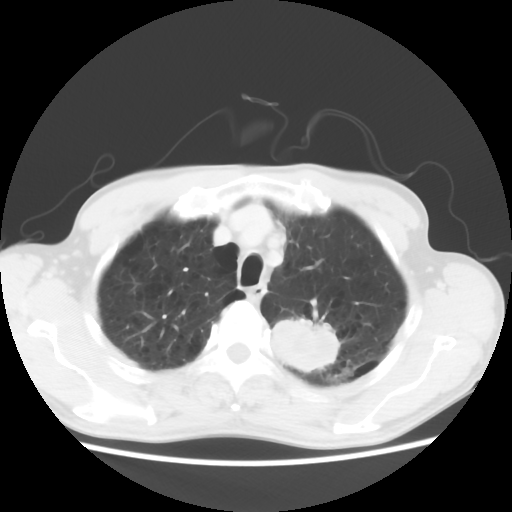
Chest CT, one axial slice; position 52 of 64 along the scan axis; 120 kVp; lung window (W 1500 / L -600 HU); 5 mm slice thickness; 512 × 512 image matrix, field of view 346 × 346 mm. Male patient, age 63 years. From the clinical record (not read from this slice): clinical TNM (as recorded): T2 N0 M0.
Annotated regions visible in this slice (bounding box drawn by a radiologist):
- lung tumour (recorded histology: adenocarcinoma): bounding box <268,309,348,382> (left, top, right, bottom; pixels)